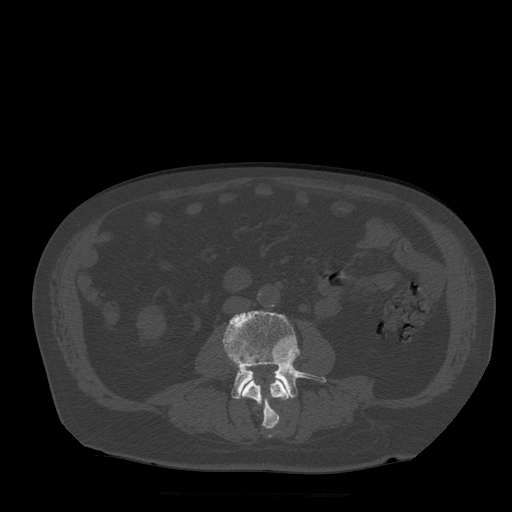
CT including the spine, one axial slice. Position 126 of 522 along the scan axis. Bone window (W 1800 / L 400 HU). 512 × 512 image matrix. Patient age 72 years. Case-level facts recorded for this patient, not image findings: primary cancer: prostate.
Annotated regions visible in this slice (semi-automatic segmentation, software-assisted and operator-edited):
- L3 vertebra: bounding box (x1, y1, x2, y2) in pixels: (240, 379, 291, 438)
- L4 vertebra: (223, 311, 326, 399)